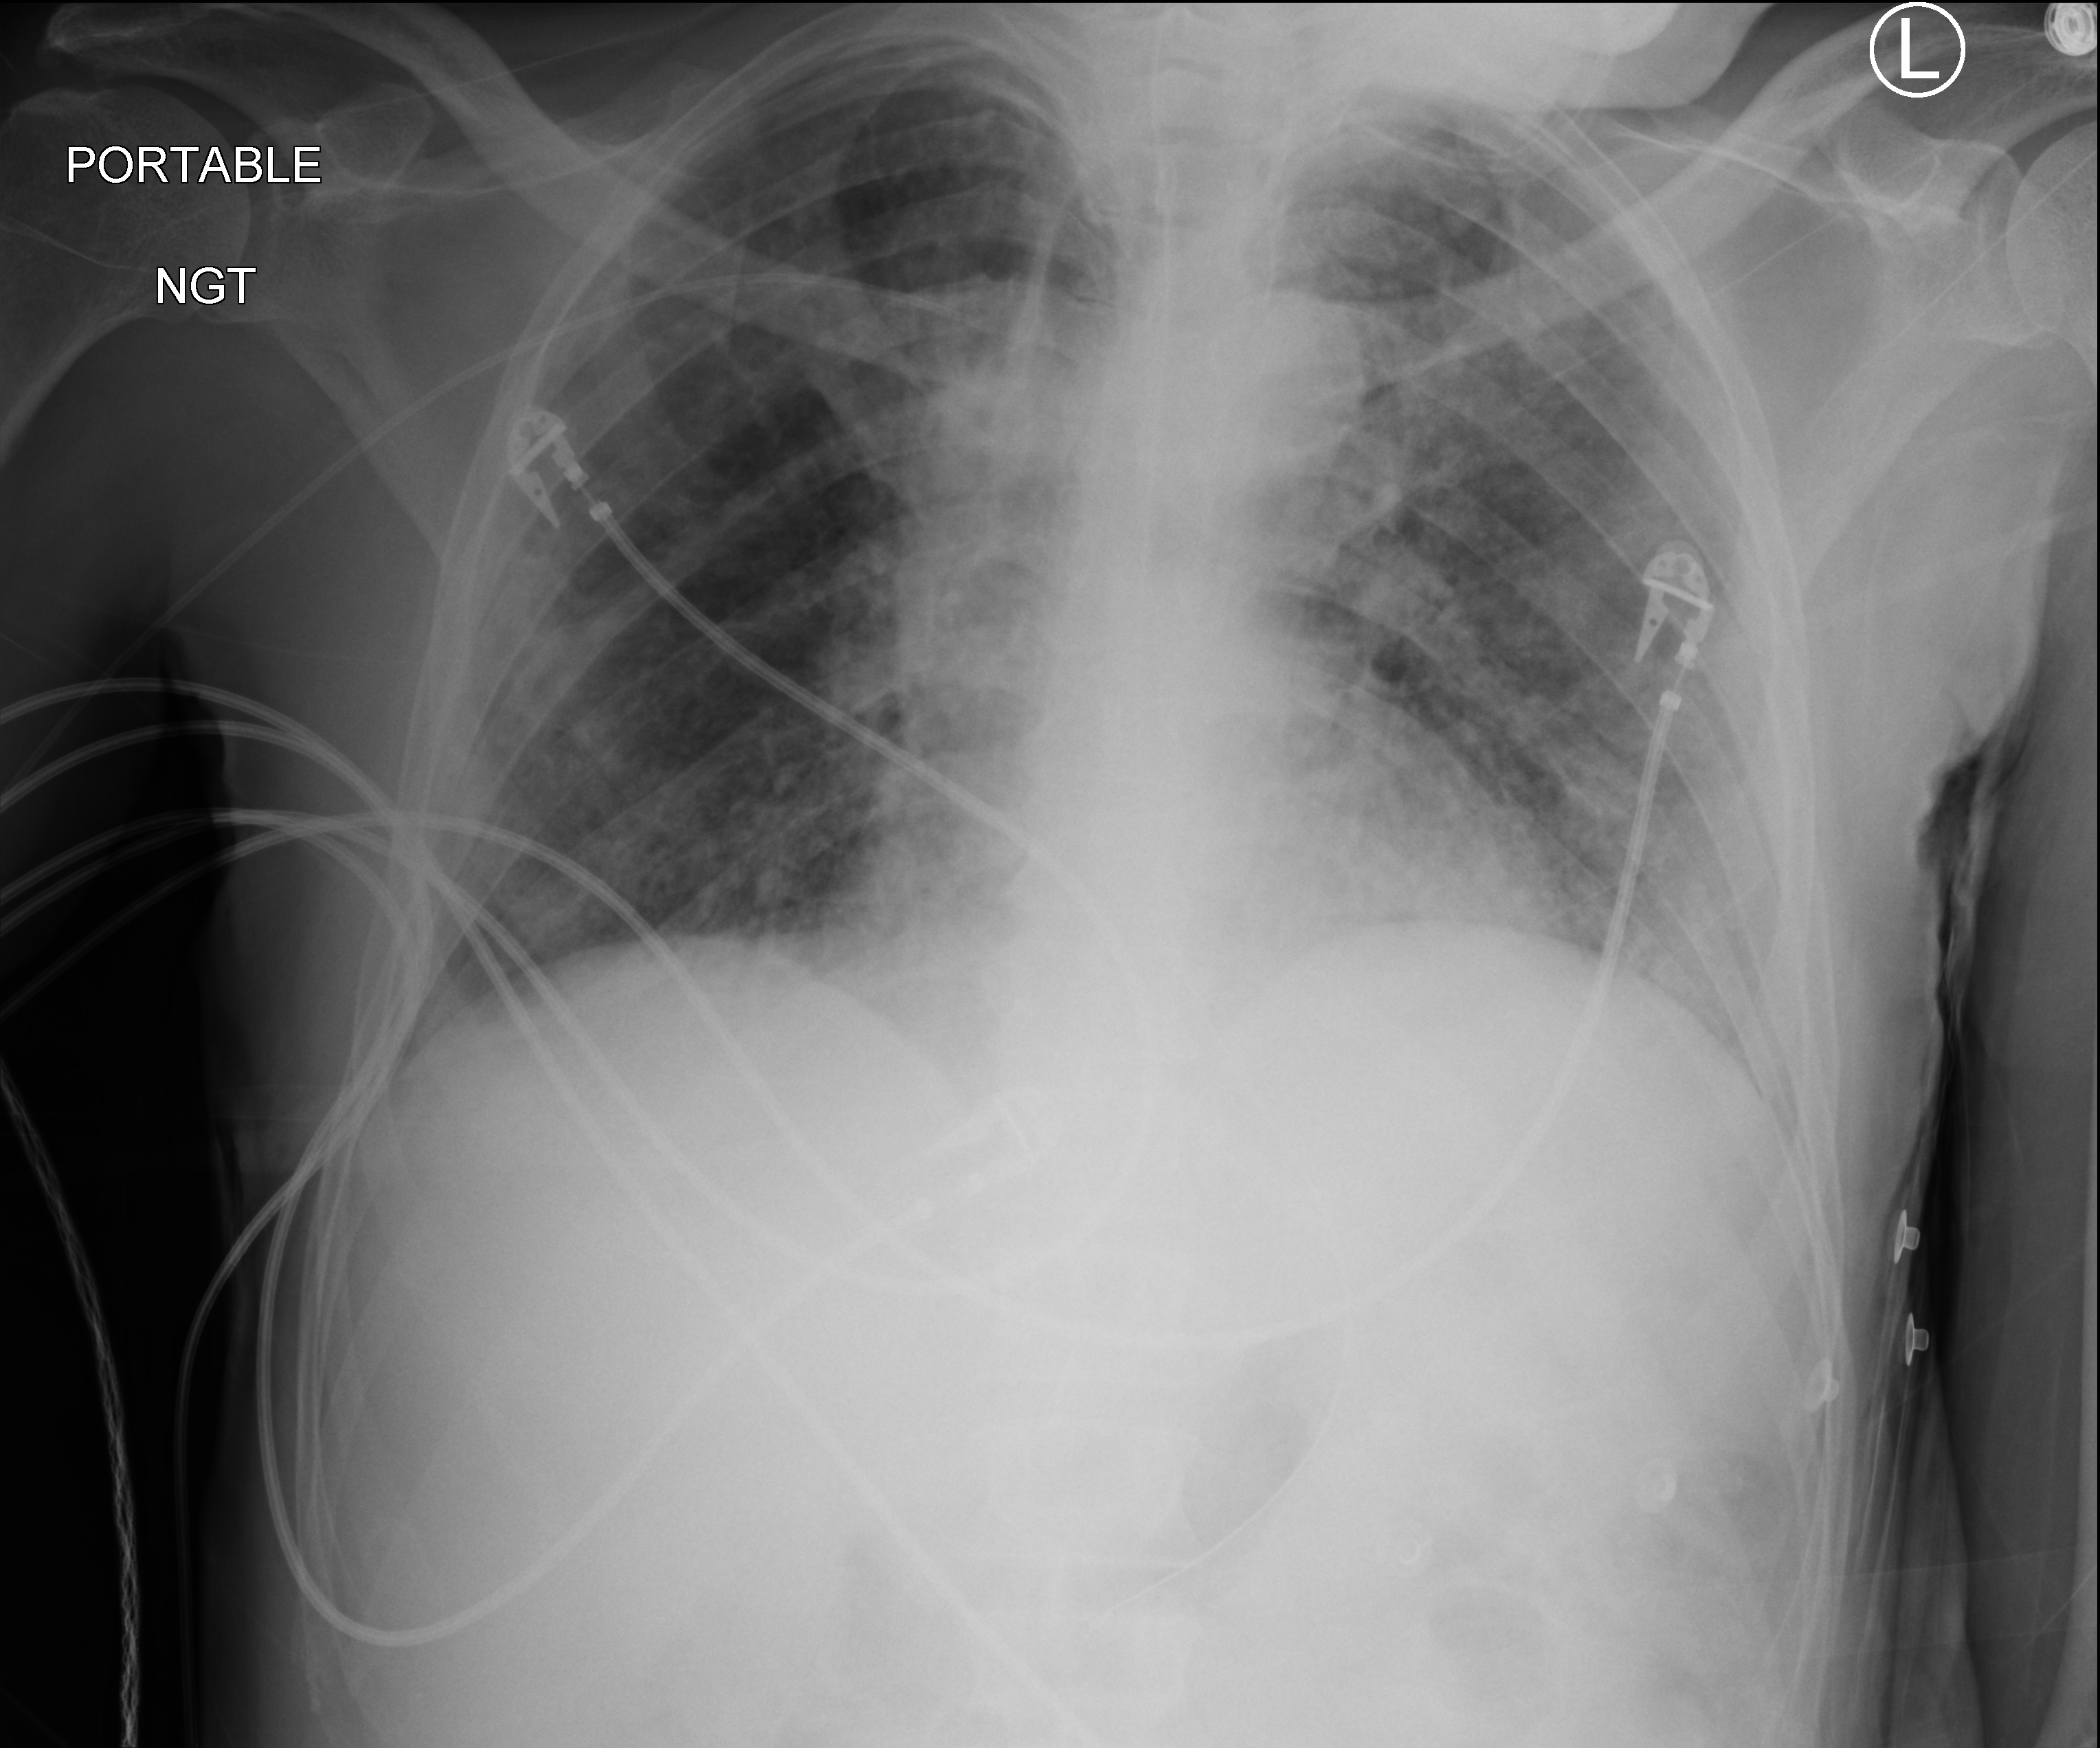
Portable chest radiograph; anteroposterior (AP) projection. Male patient hospitalised with COVID-19, age 18–59 years.
Hospital-stay facts (about this admission, not read from this image; timing relative to this image not recorded): admitted to intensive care during this hospital stay: yes; length of hospital stay: 41 days; COPD (admission record): no.